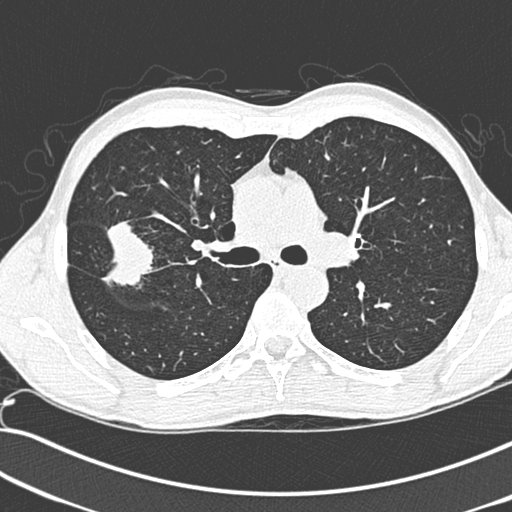
Low-dose screening chest CT, one axial slice; slice 190 of 281 in the series (ordered by position); 120 kVp; lung window (W 1500 / L -600 HU); 1.3 mm slice thickness; 512 × 512 image matrix, field of view 341 × 341 mm.
Outlined on this slice (outlined manually by an expert reader):
- lesion 1 (tumor, upper lobe of right lung): bounding box [x1, y1, x2, y2] px = [102, 221, 153, 286]